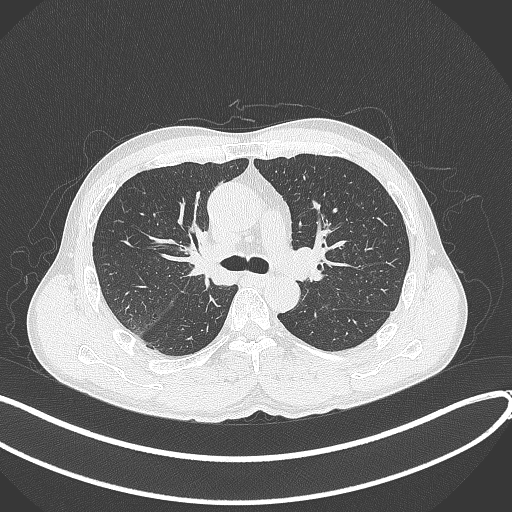
Chest CT, one axial slice. Slice 246 of 409 in the series (ordered by position). Lung window (W 1500 / L -600 HU). 512 × 512 image matrix. Male patient, age 53 years. From the clinical record (not read from this slice): clinical TNM (as recorded): T1b N0 M0.
Structures marked on this image (bounding box drawn by a radiologist):
- lung tumour (recorded histology: squamous cell carcinoma): bounding box <181,221,236,290> (left, top, right, bottom; pixels)